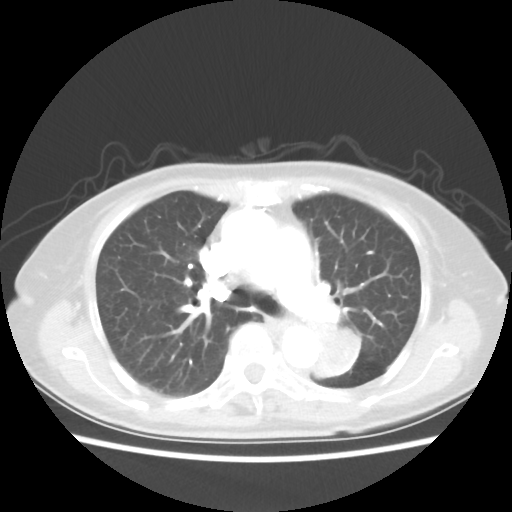
Chest CT, one axial slice. Position 31 of 50 along the scan axis. Reconstruction kernel STANDARD. 80 kVp. Lung window (W 1500 / L -600 HU). 512 × 512 image matrix, field of view 335 × 335 mm. Patient: female, 81 years. Case-level facts recorded for this patient, not image findings: clinical TNM (as recorded): T2 N0 M1a.
Outlined on this slice (rectangle marked by the reading radiologist):
- lung tumour (recorded histology: squamous cell carcinoma): box from (x=309, y=317) to (x=361, y=382) px